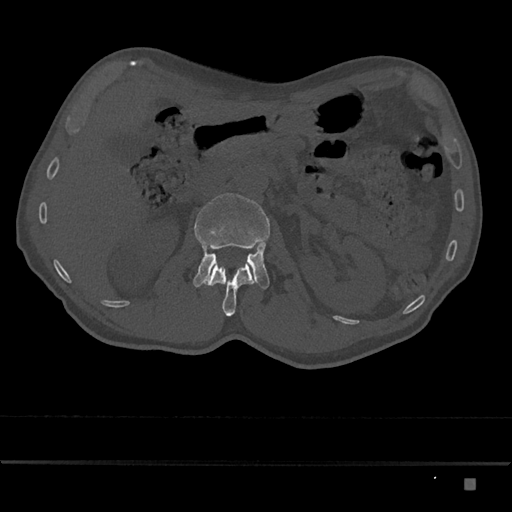
CT including the spine, one axial slice; slice 509 of 797 in the series (ordered by position); reconstruction kernel Br40s/3; bone window (W 1800 / L 400 HU); 512 × 512 image matrix. Male patient, age 72 years. From the clinical record (not read from this slice): primary cancer: prostate.
Annotated regions visible in this slice (semi-automatically segmented with operator editing):
- L1 vertebra: bounding box [x1, y1, x2, y2] px = [206, 263, 255, 317]
- L2 vertebra: [193, 193, 270, 289]